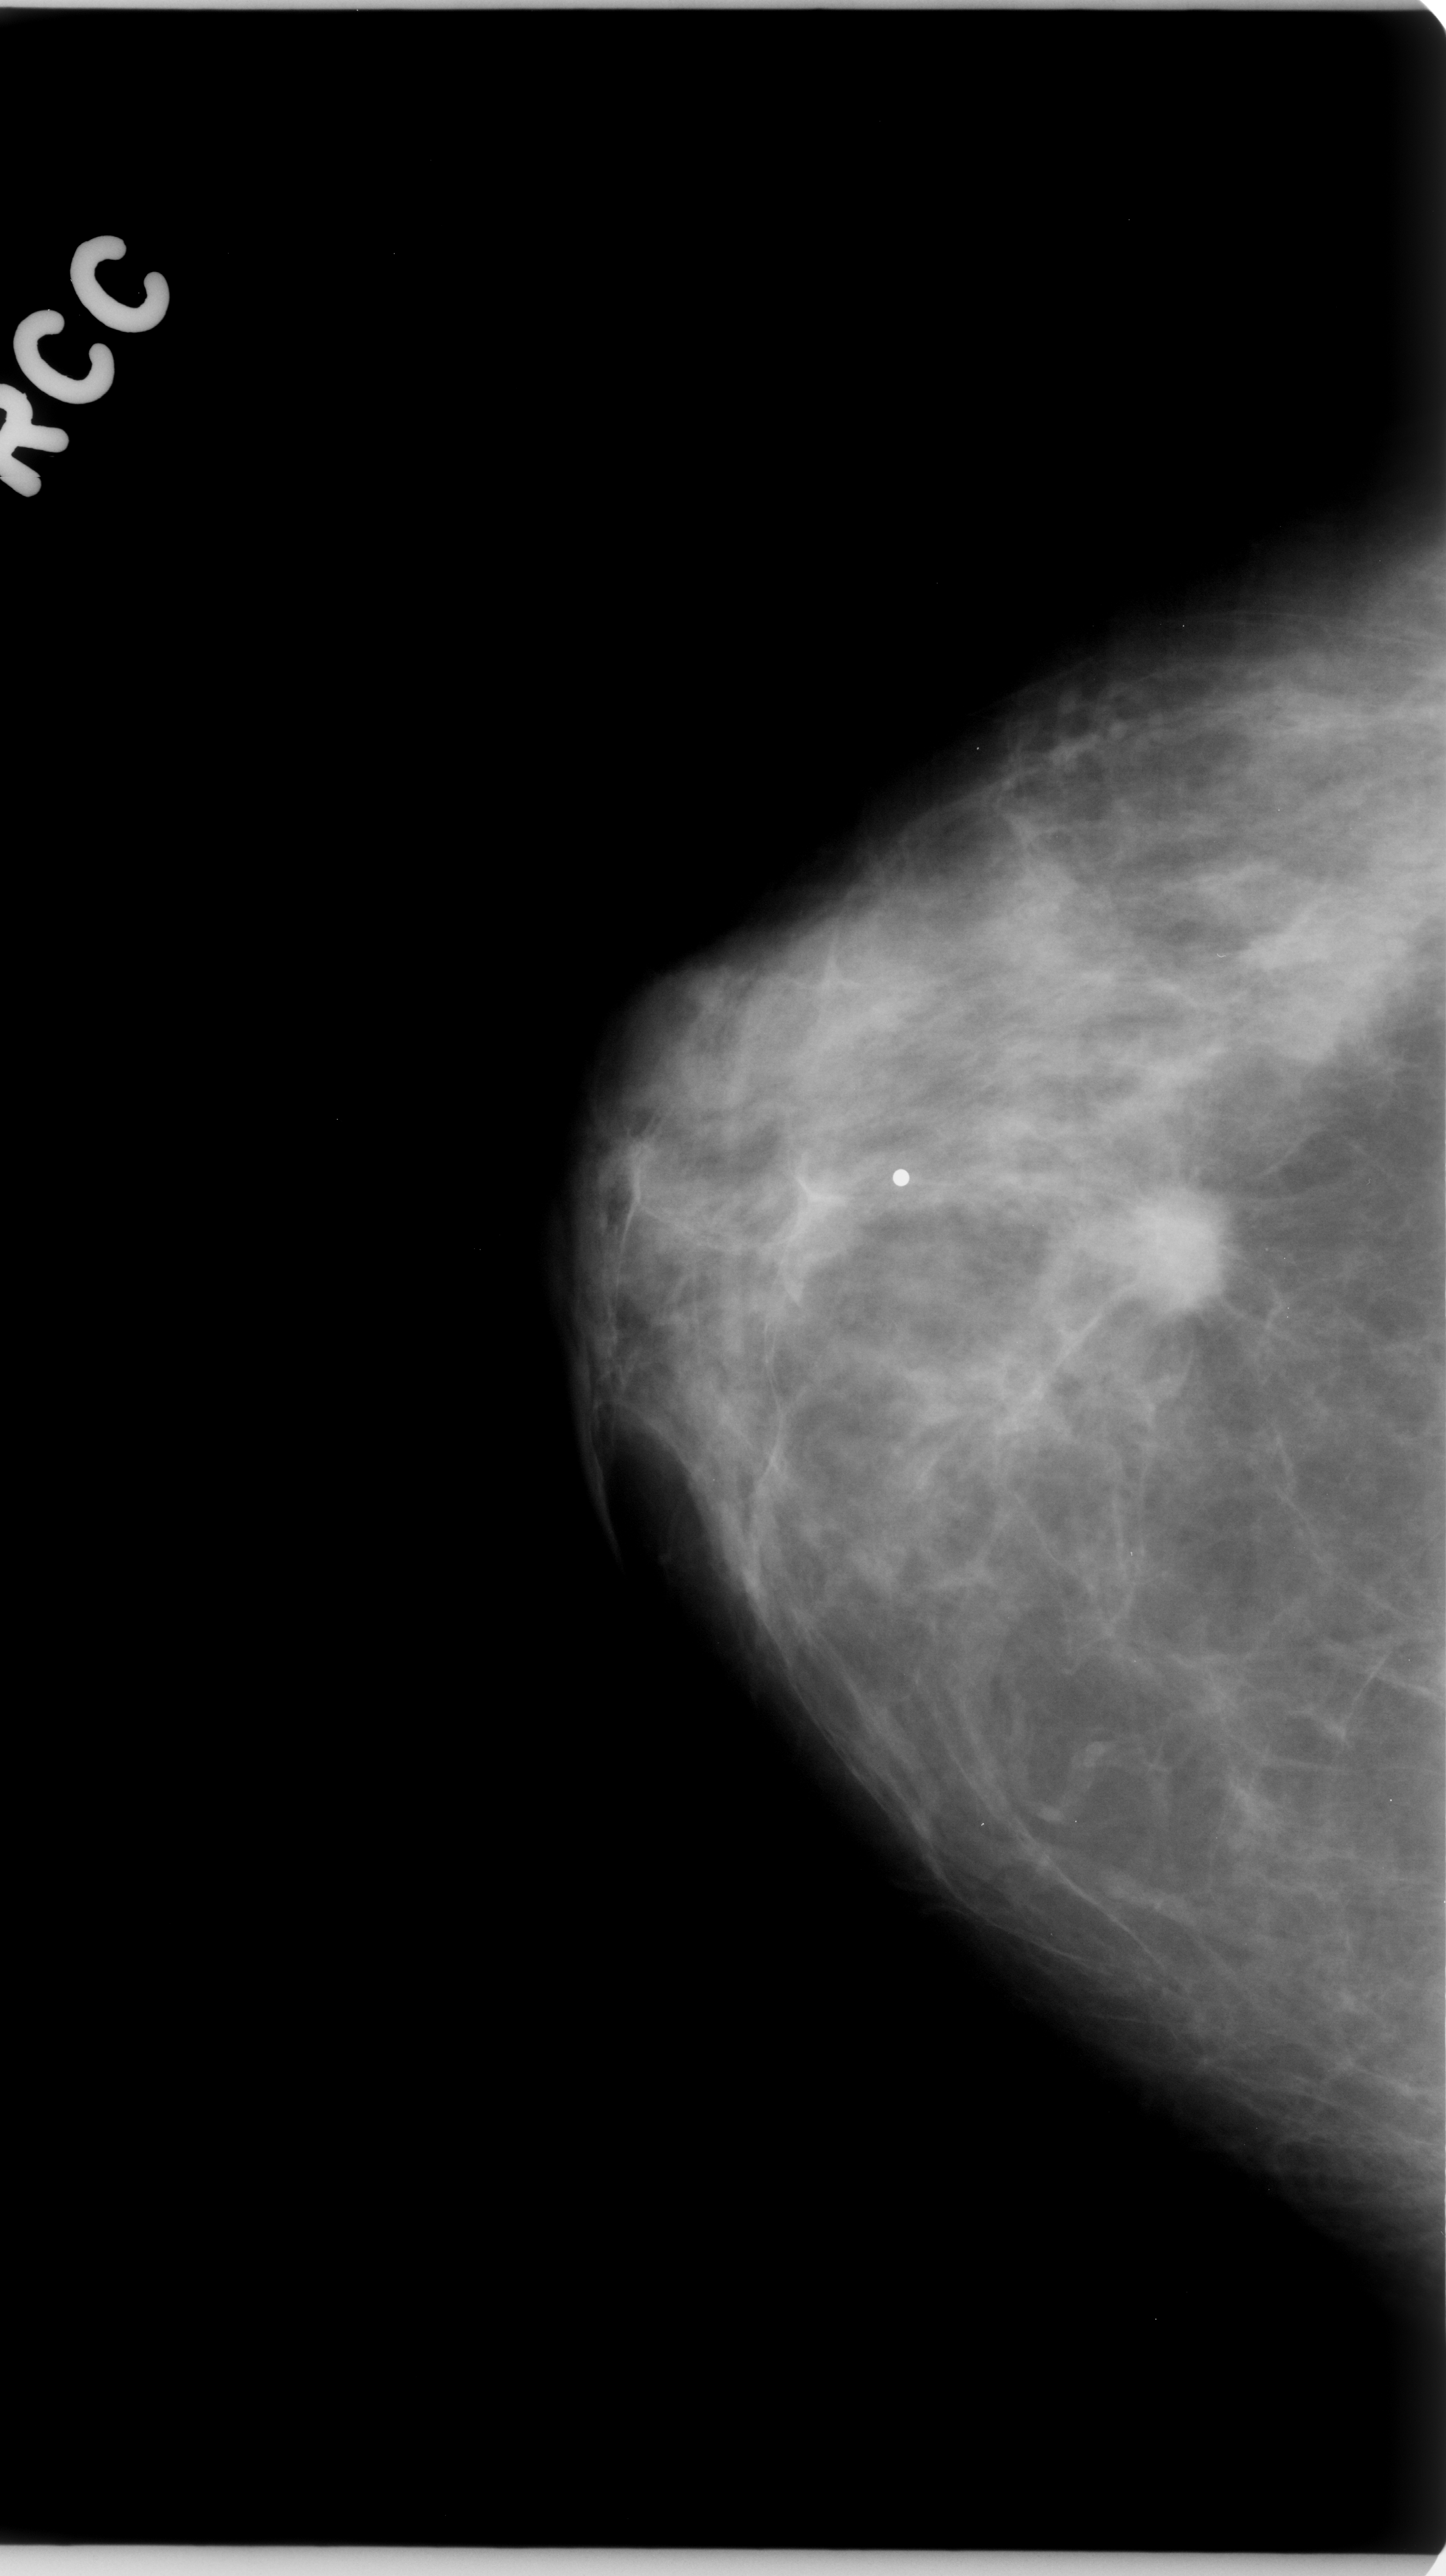
Mammogram (digitized film); right breast; craniocaudal (CC) view; breast composition: scattered fibroglandular densities (BI-RADS density category 2 of 4); 1446 × 2576 image matrix.
Expert-marked regions of interest on this image (one box per marked abnormality):
- mass, shape irregular, margins spiculated; BI-RADS assessment category 5; subtlety rating 5 on a 1 (subtle) to 5 (obvious) scale; pathology (as recorded): malignant: box from (x=1056, y=1135) to (x=1250, y=1330) px